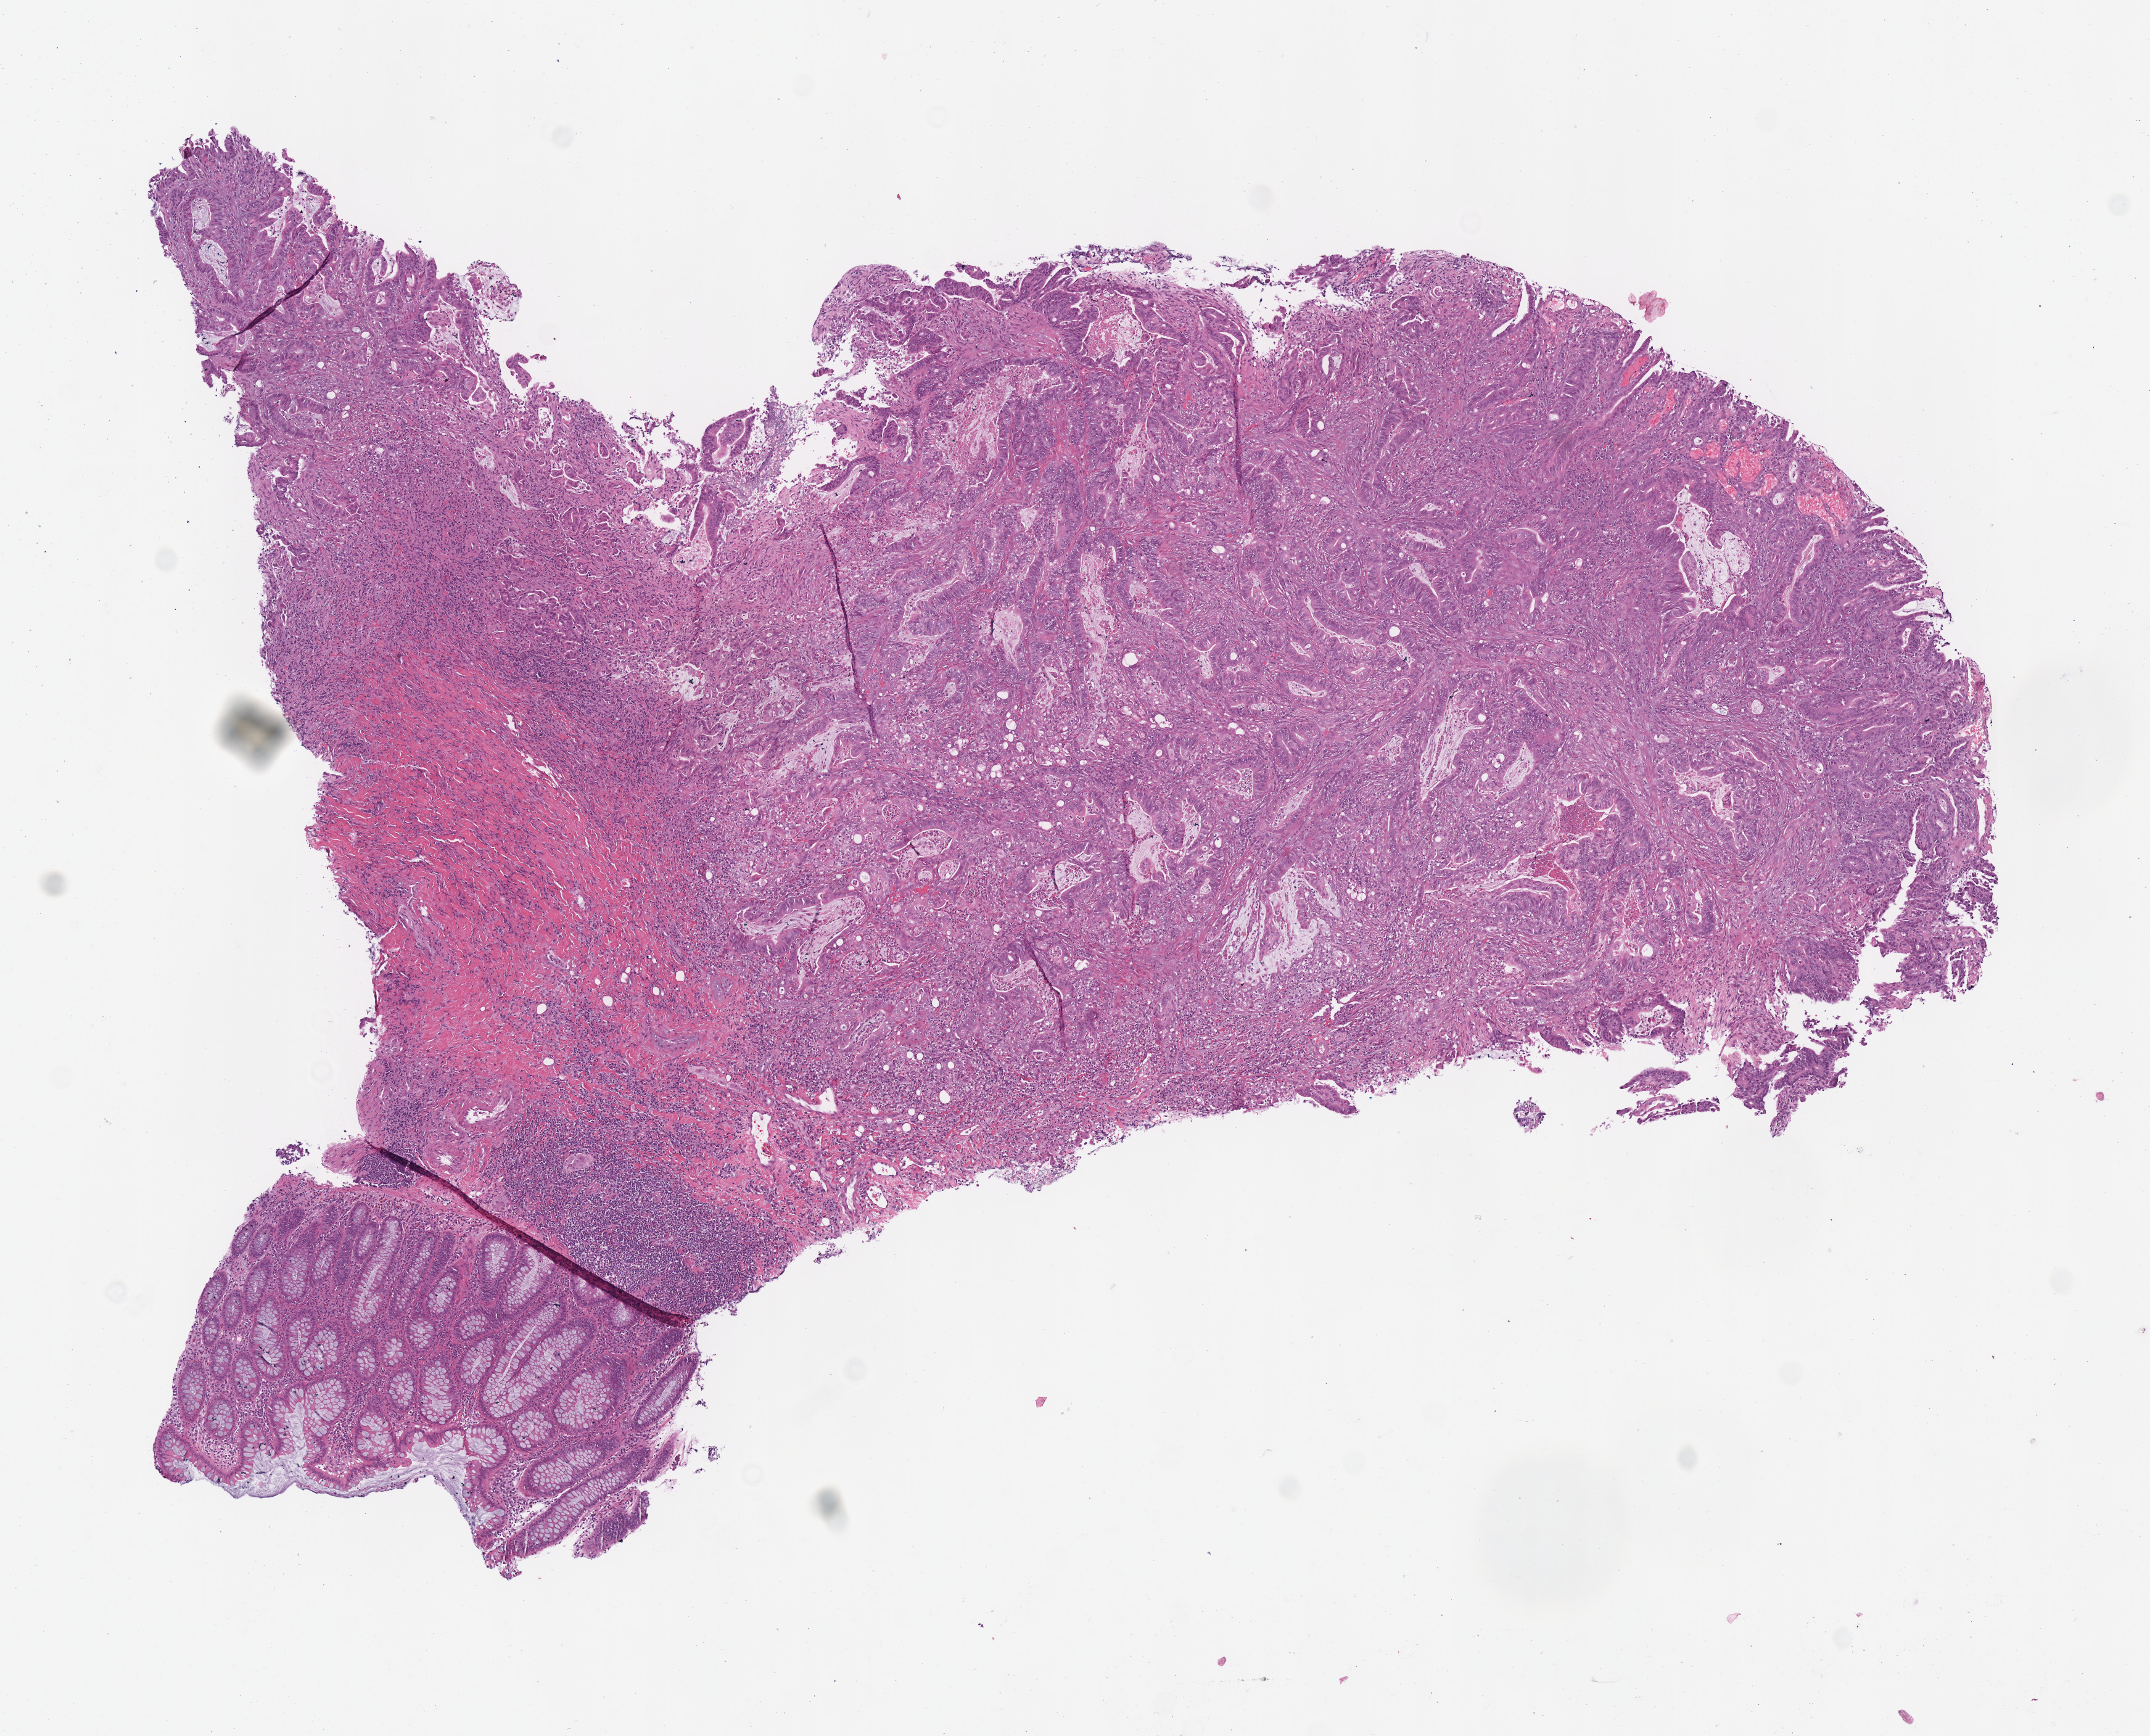
Digitized H&E tissue section (whole slide), a low-resolution overview of the entire scanned area, about 6.9 x 5.5 mm, frozen section from the top of the tissue portion, primary tumour sample from the colon. Female, age 80 years at initial diagnosis. Slide review estimates, as recorded: tumour cells 83%, tumour nuclei 80%, normal cells 0%, stromal cells 0%, necrosis 17%. Inflammatory infiltration, as recorded: lymphocyte infiltration 10%, monocyte infiltration 2%, neutrophil infiltration 5%.
AJCC pathologic stage: IIA. Pathologic diagnosis: Adenocarcinoma, NOS.